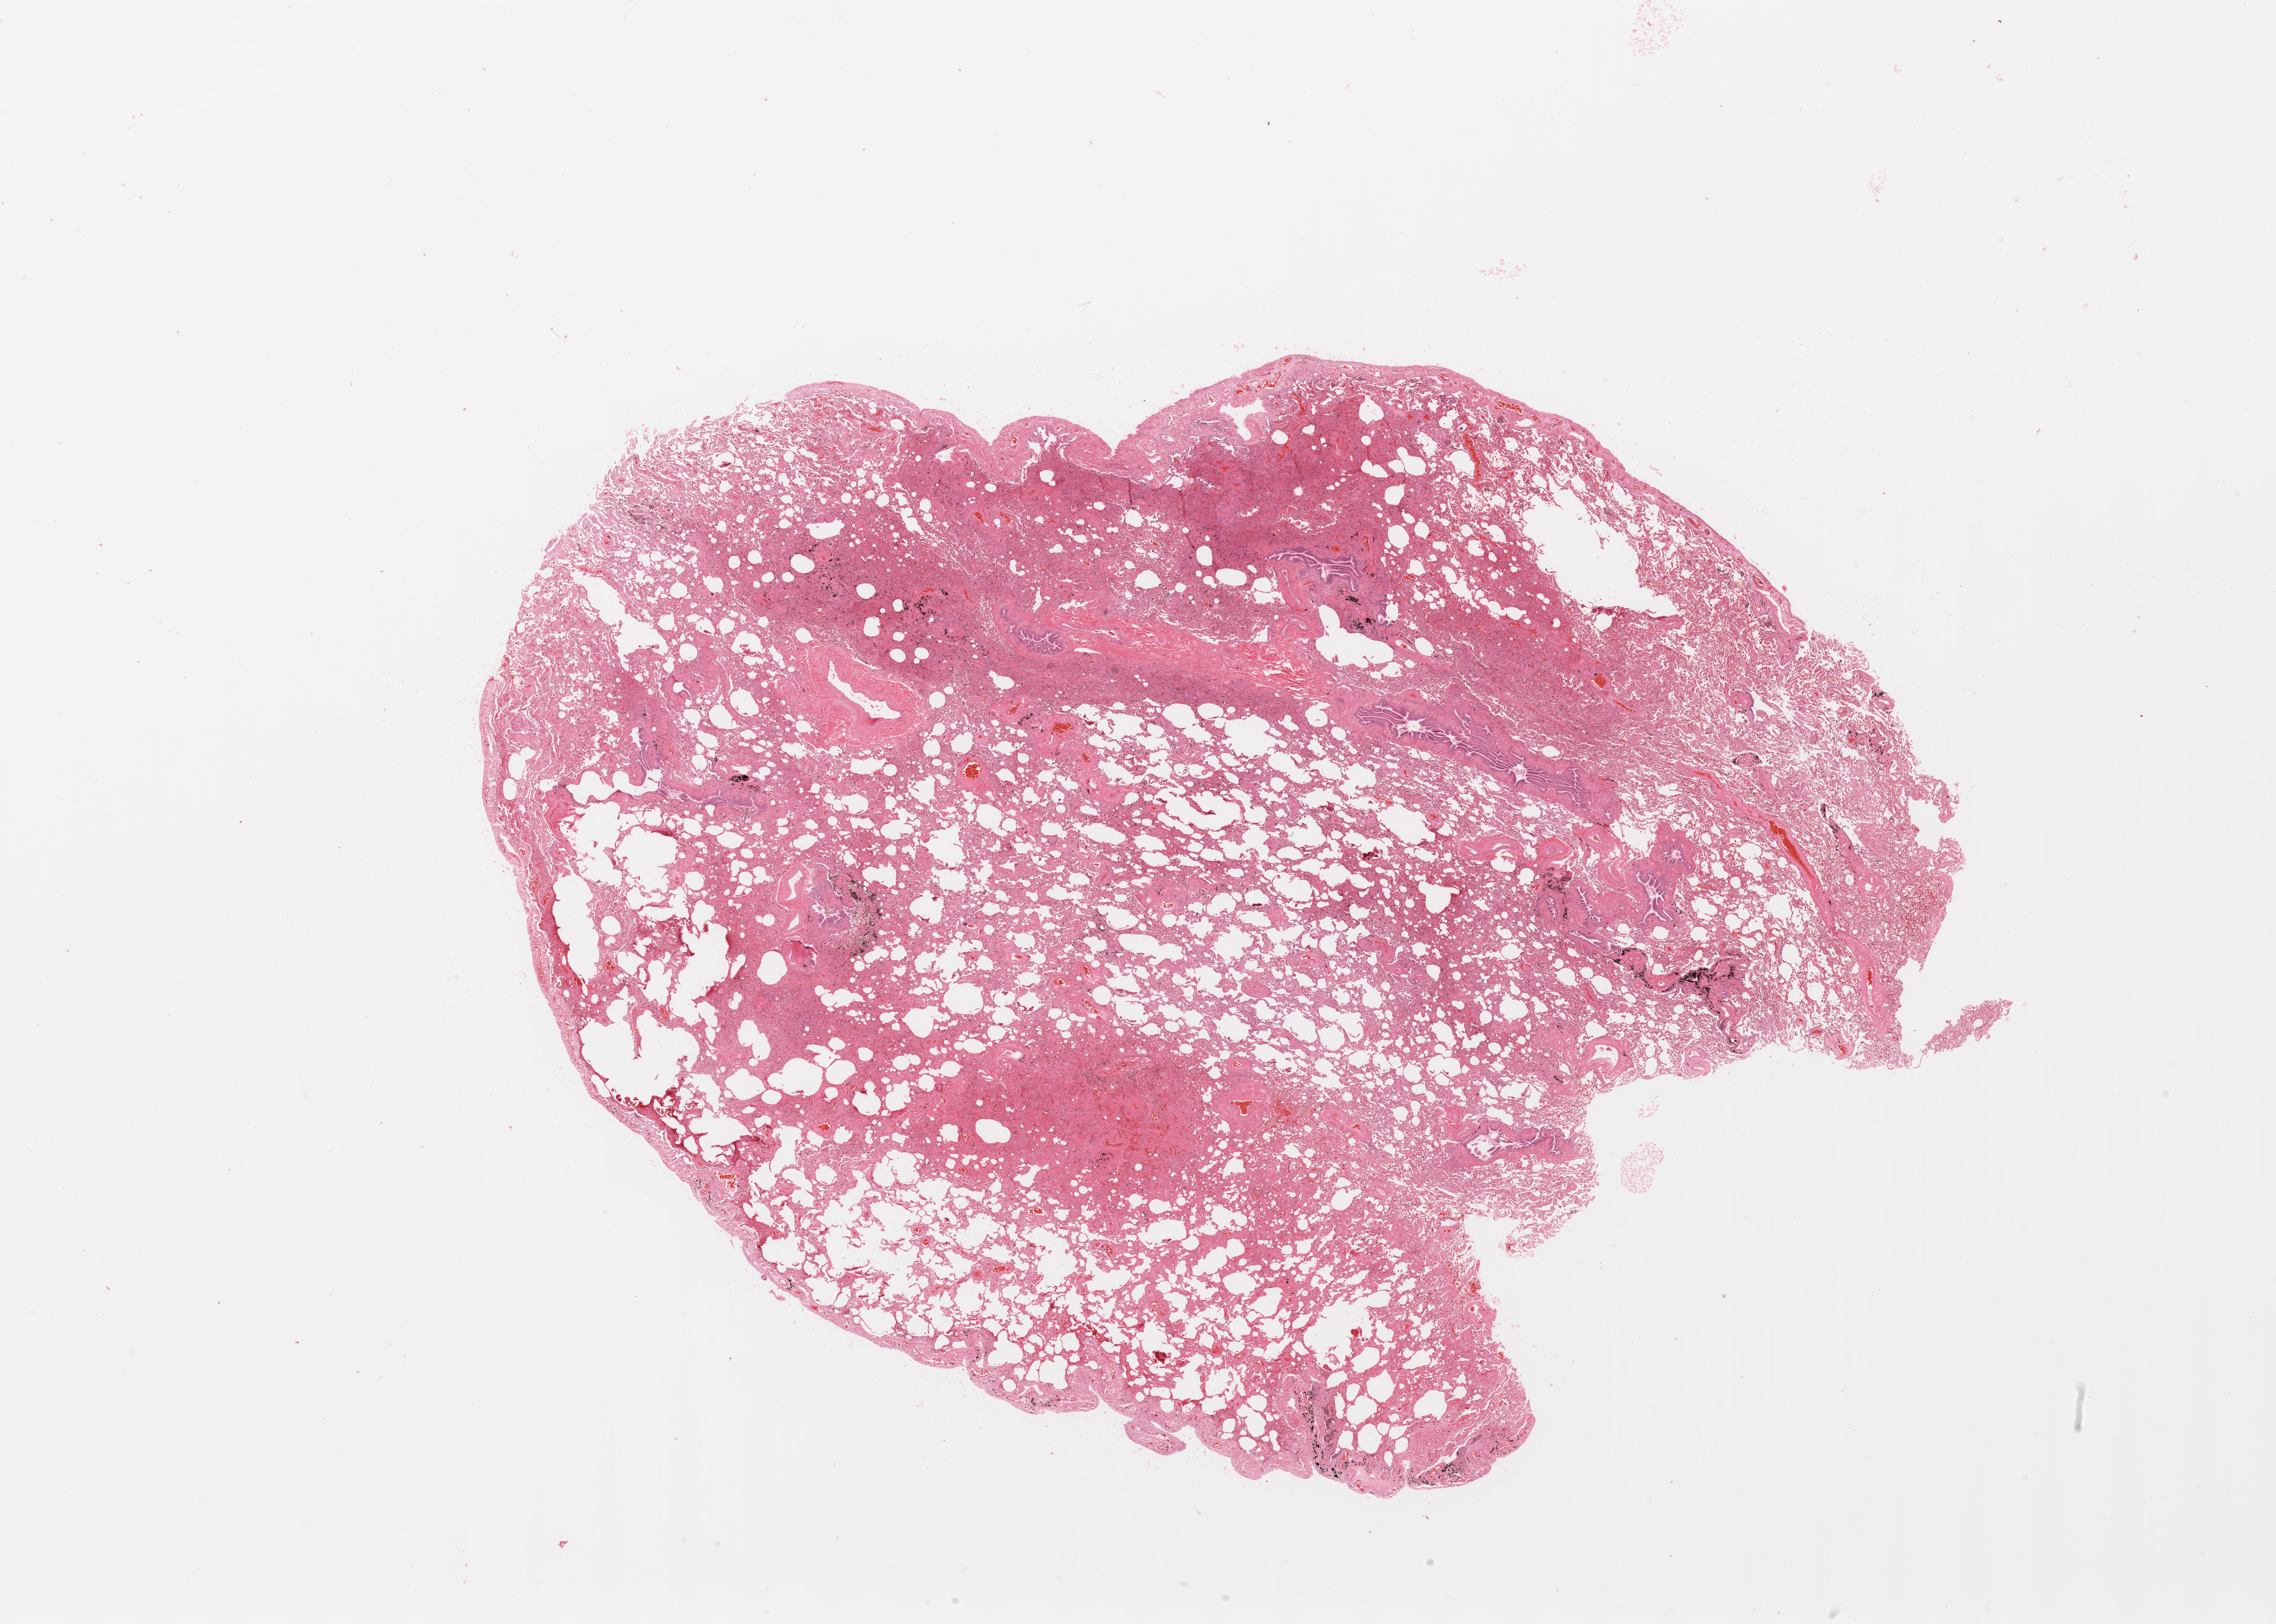
H&E-stained whole-slide image, low-resolution overview of the scanned area, about 29.5 x 21.1 mm, normal (non-tumour) tissue sample, sampled site: lung. 71-year-old male patient.
This section: normal (non-tumour) tissue from the same patient. Patient diagnosis: Adenocarcinoma, NOS.